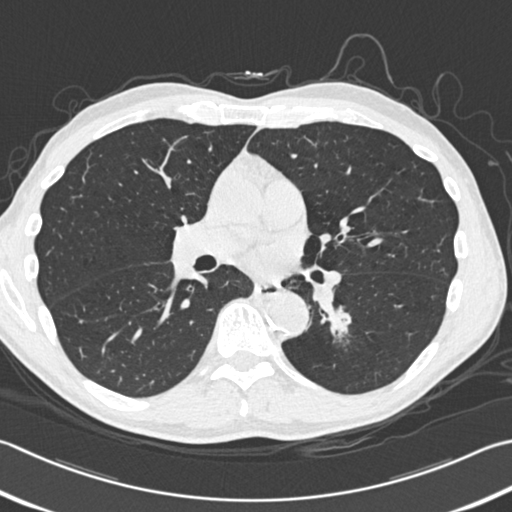
Low-dose screening chest CT, one axial slice. Slice 190 of 354 in the series (ordered by position). Lung window (W 1500 / L -600 HU). 1 mm slice thickness. 512 × 512 image matrix, field of view 346 × 346 mm.
Annotated regions visible in this slice (manually delineated by an expert):
- lesion 1 (tumor, lower lobe of left lung): bounding box <337,310,350,326> (left, top, right, bottom; pixels)